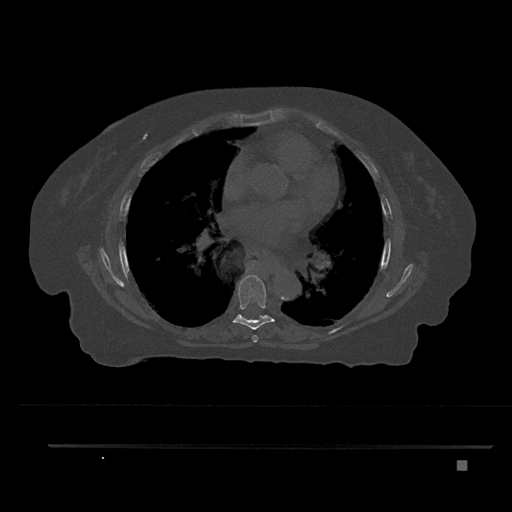
CT including the spine, one axial slice. Slice 486 of 797 in the series (ordered by position). Reconstruction kernel Br40s/3. 120 kVp. Bone window (W 1800 / L 400 HU). 512 × 512 image matrix. Female patient, age 76 years. Case-level facts recorded for this patient, not image findings: primary cancer: lung; vertebrae with lytic lesions (as recorded): T11, L3.
Outlined on this slice (semi-automatic segmentation, software-assisted and operator-edited):
- T6 vertebra: box from (x=252, y=335) to (x=258, y=343) px
- T7 vertebra: (x=232, y=274)–(x=275, y=330)
- T8 vertebra: (x=240, y=315)–(x=268, y=320)